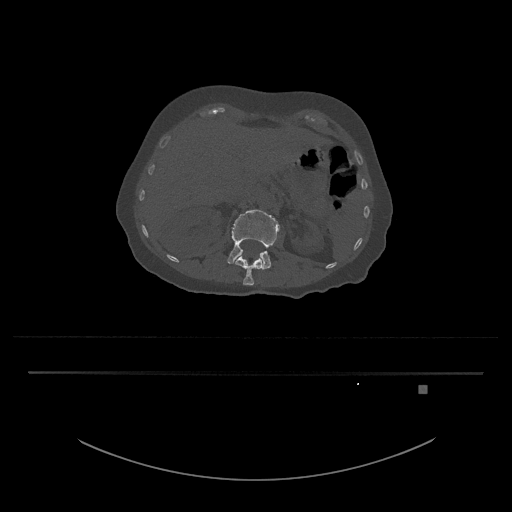
CT including the spine, one axial slice. Slice 519 of 797 in the series (ordered by position). Reconstruction kernel Br40s/3. Bone window (W 1800 / L 400 HU). 512 × 512 image matrix, field of view 500 × 500 mm. Female patient, age 57 years. Case-level facts recorded for this patient, not image findings: primary cancer: cervical.
Structures marked on this image (semi-automatically segmented with operator editing):
- L1 vertebra: bounding box (x1, y1, x2, y2) in pixels: (235, 255, 263, 286)